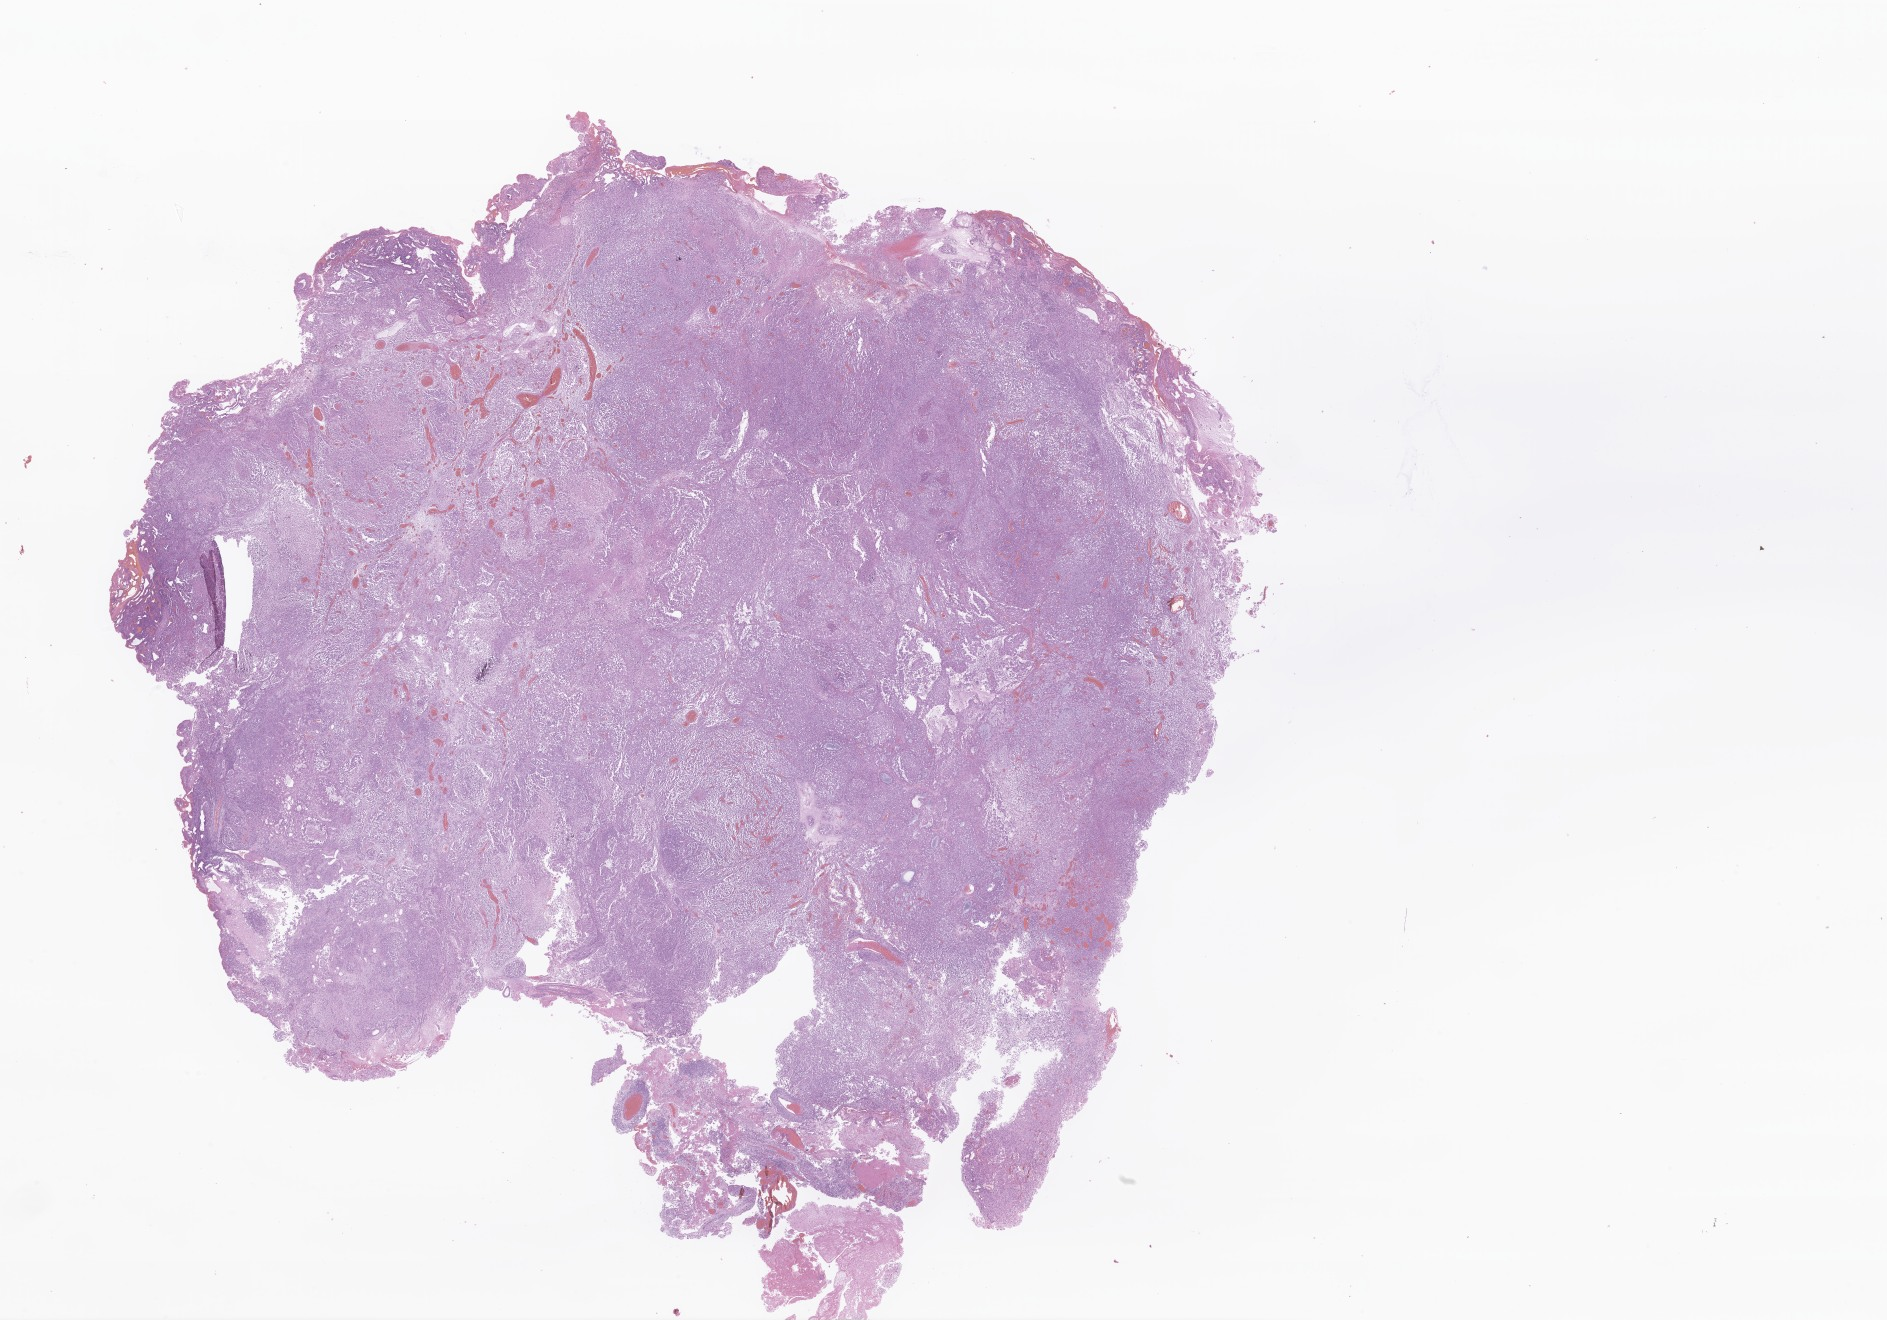
Digitized H&E-stained section of tumor tissue from the brain — shown as a low-resolution overview of the whole scanned area (about 31.8 x 22.3 mm). Formalin-fixed paraffin-embedded section. Patient: male, age 35 months (2 years 11 months).
- diagnosis: Atypical teratoid/rhabdoid tumor